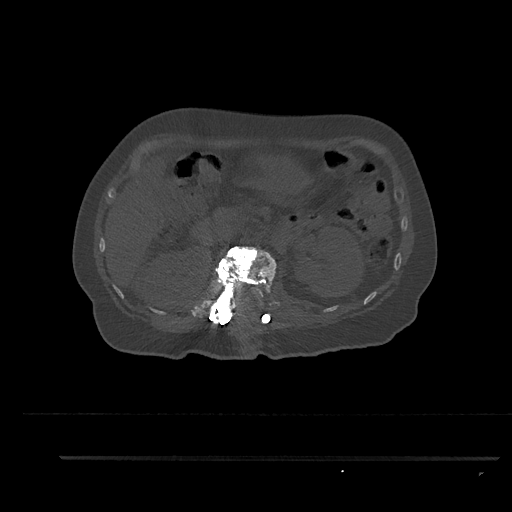
CT including the spine, one axial slice. Slice 216 of 797 in the series (ordered by position). Reconstruction kernel Br40s/3. 120 kVp. Bone window (W 1800 / L 400 HU). 0.5 mm slice thickness. 512 × 512 image matrix, field of view 408 × 408 mm. Female patient, age 44 years. Case-level facts recorded for this patient, not image findings: primary cancer: renal; vertebrae with lytic lesions (as recorded): L1.
Outlined on this slice (semi-automatically segmented with operator editing):
- L1 vertebra: bounding box <207,246,277,321> (left, top, right, bottom; pixels)